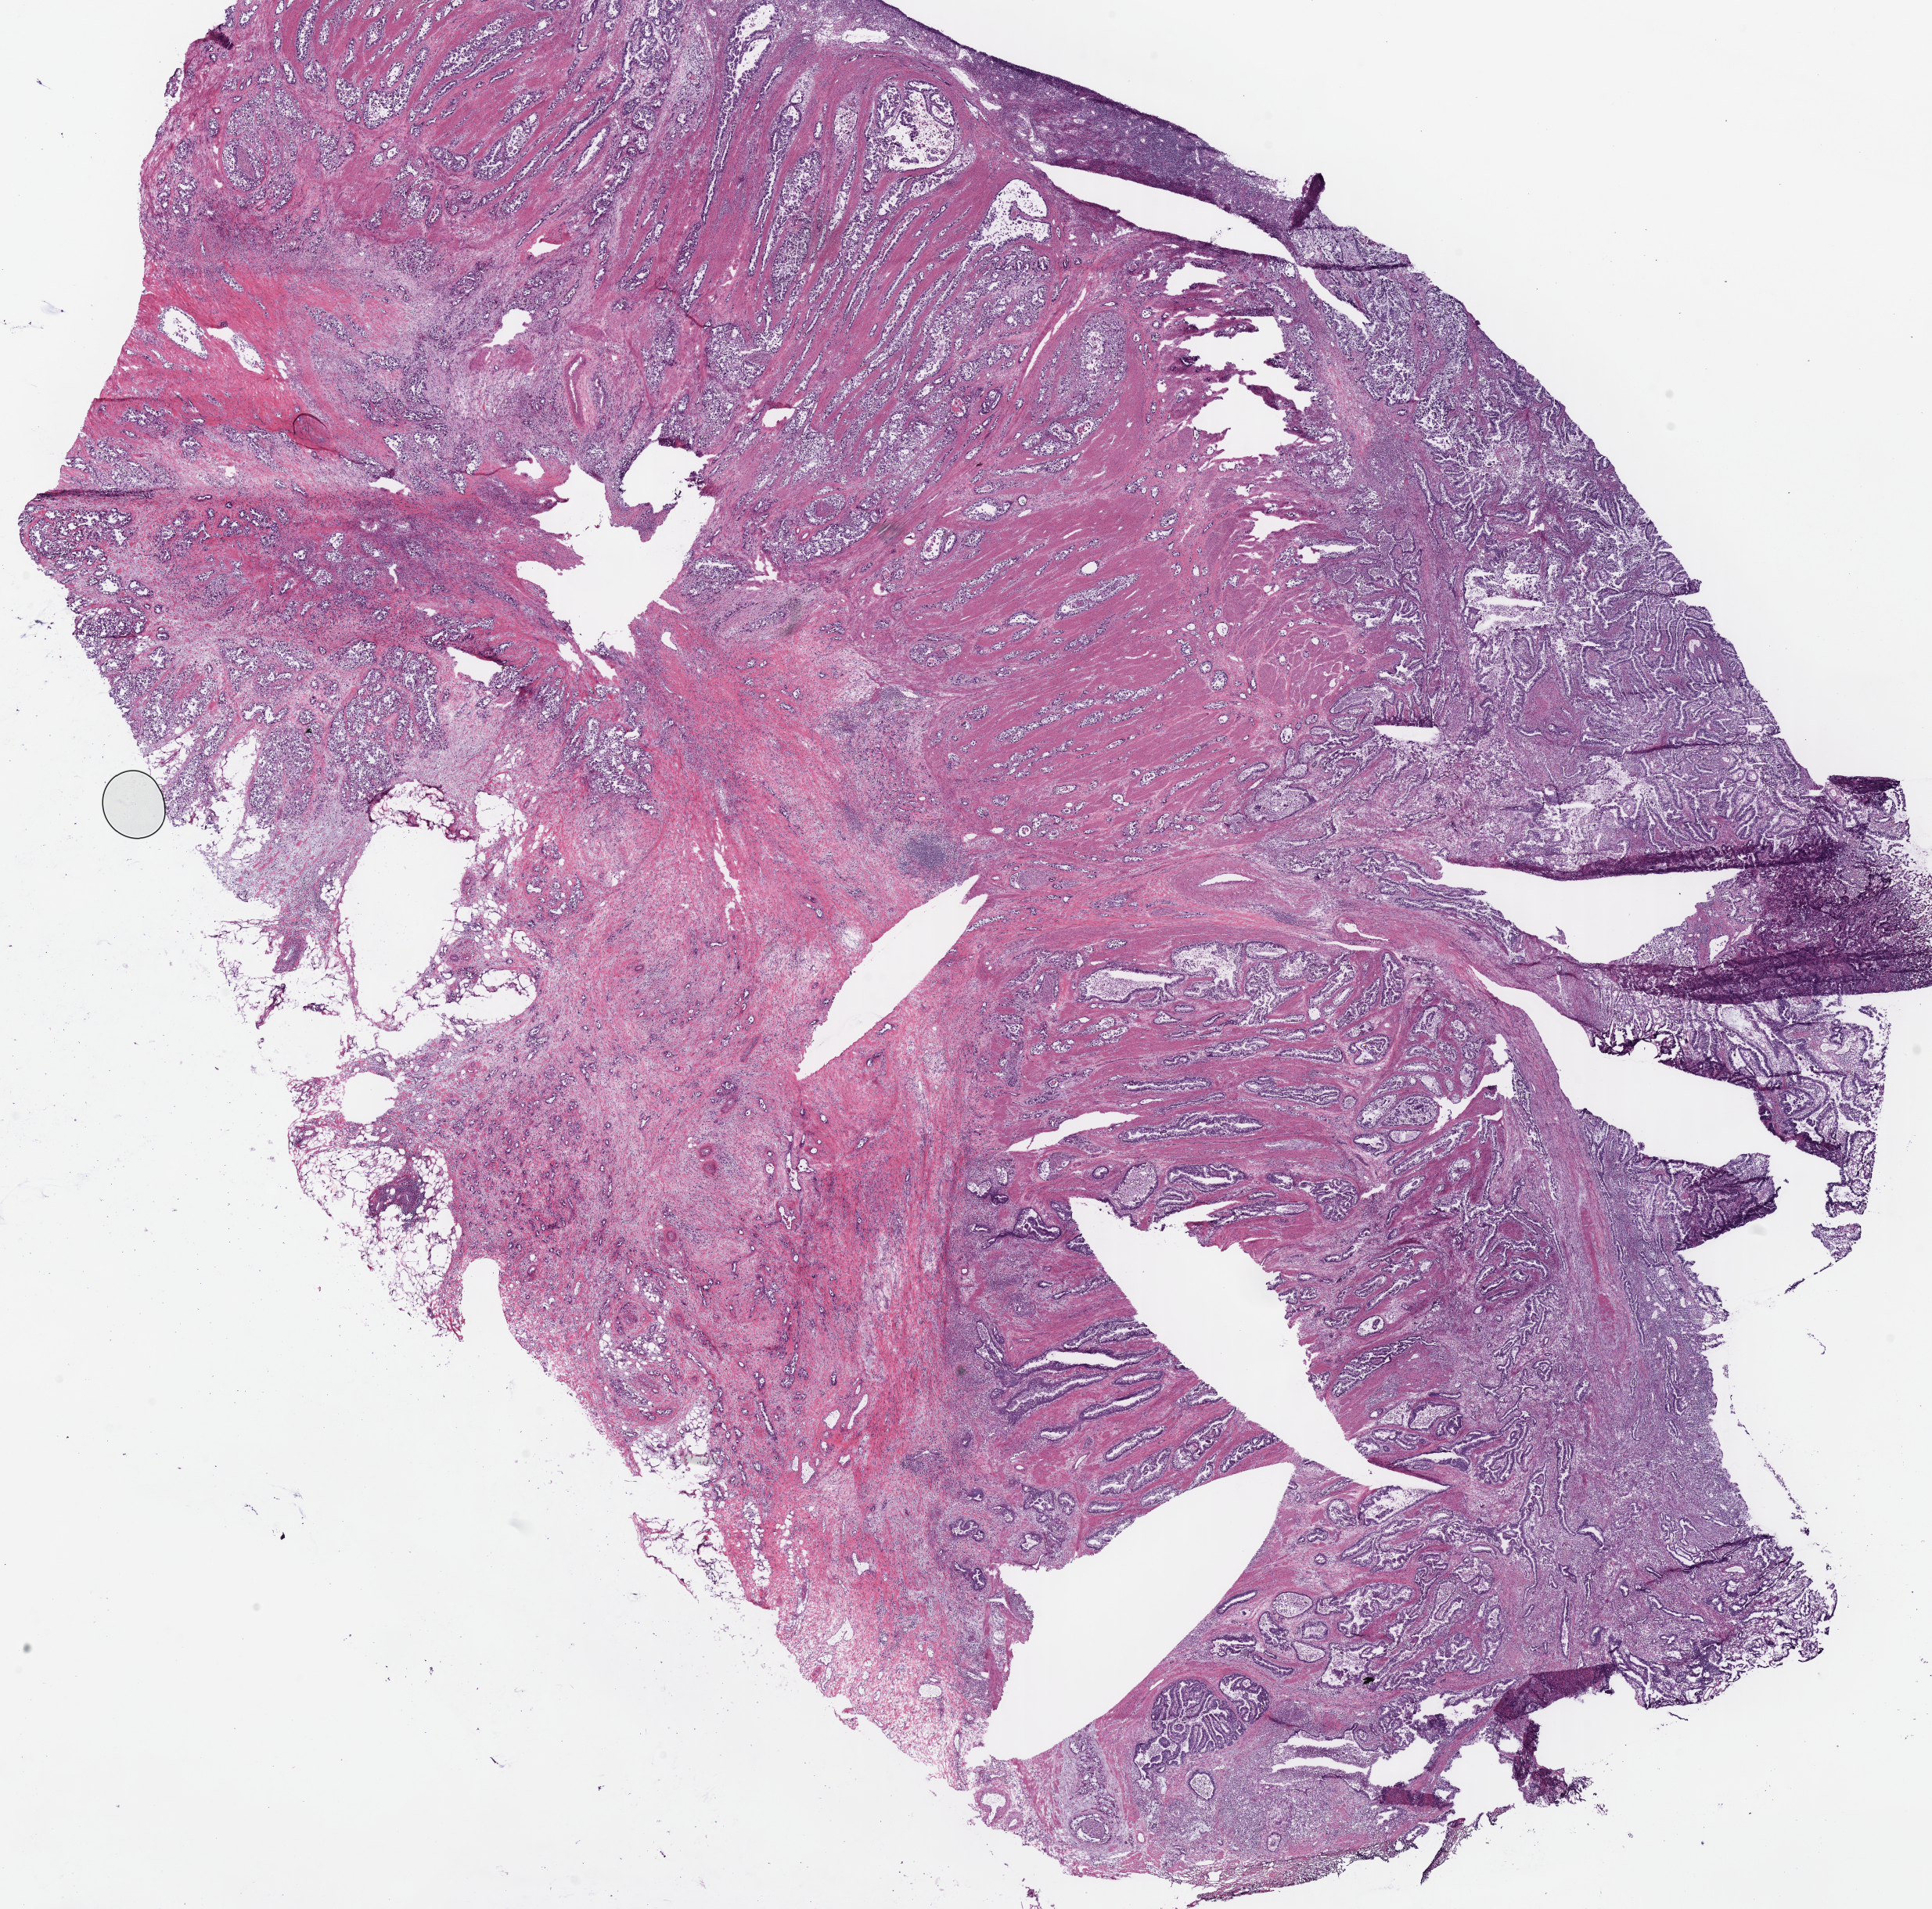
H&E-stained whole-slide image, low-resolution overview of the scanned area, about 19.5 x 19.2 mm (slide scanned at 40x), frozen section from the bottom of the tissue portion, sample: primary tumour, stomach. Male patient; age at initial diagnosis 74 years. Histologic grade: G2 (moderately differentiated). Composition of this section per pathologist review: tumour cells 50%, tumour nuclei 60%, normal cells 0%, stromal cells 50%, necrosis 0%.
AJCC pathologic stage: IIB (7th edition). Pathologic diagnosis: Adenocarcinoma, NOS (cardia, NOS). Lymph nodes positive (case pathology): 2 of 15 examined.